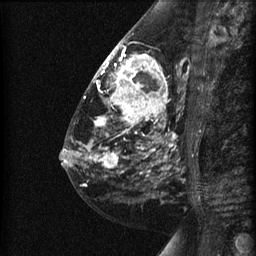
Breast MRI (dynamic contrast-enhanced), one sagittal slice. Dynamic contrast-enhanced series, image 2 of 3 at this slice position (ordered by acquisition). 1.5 T. TE 4.2 ms, TR 22.7 ms. 1.5 mm slice thickness. 256 × 256 image matrix, field of view 180 × 180 mm. Patient: female, 48 years. From the clinical record (not read from this slice): setting: breast cancer imaged before/during neoadjuvant chemotherapy; receptor status: triple-negative.
Annotated regions visible in this slice (semi-automatically segmented with operator editing):
- analysis volume of interest (the breast-tissue region the enhancement analysis was run in; not a lesion): bounding box [x1, y1, x2, y2] px = [89, 27, 191, 180]
- tumour enhancement mask (voxels above the 90 % enhancement threshold inside the analysis volume of interest): [94, 45, 175, 167]